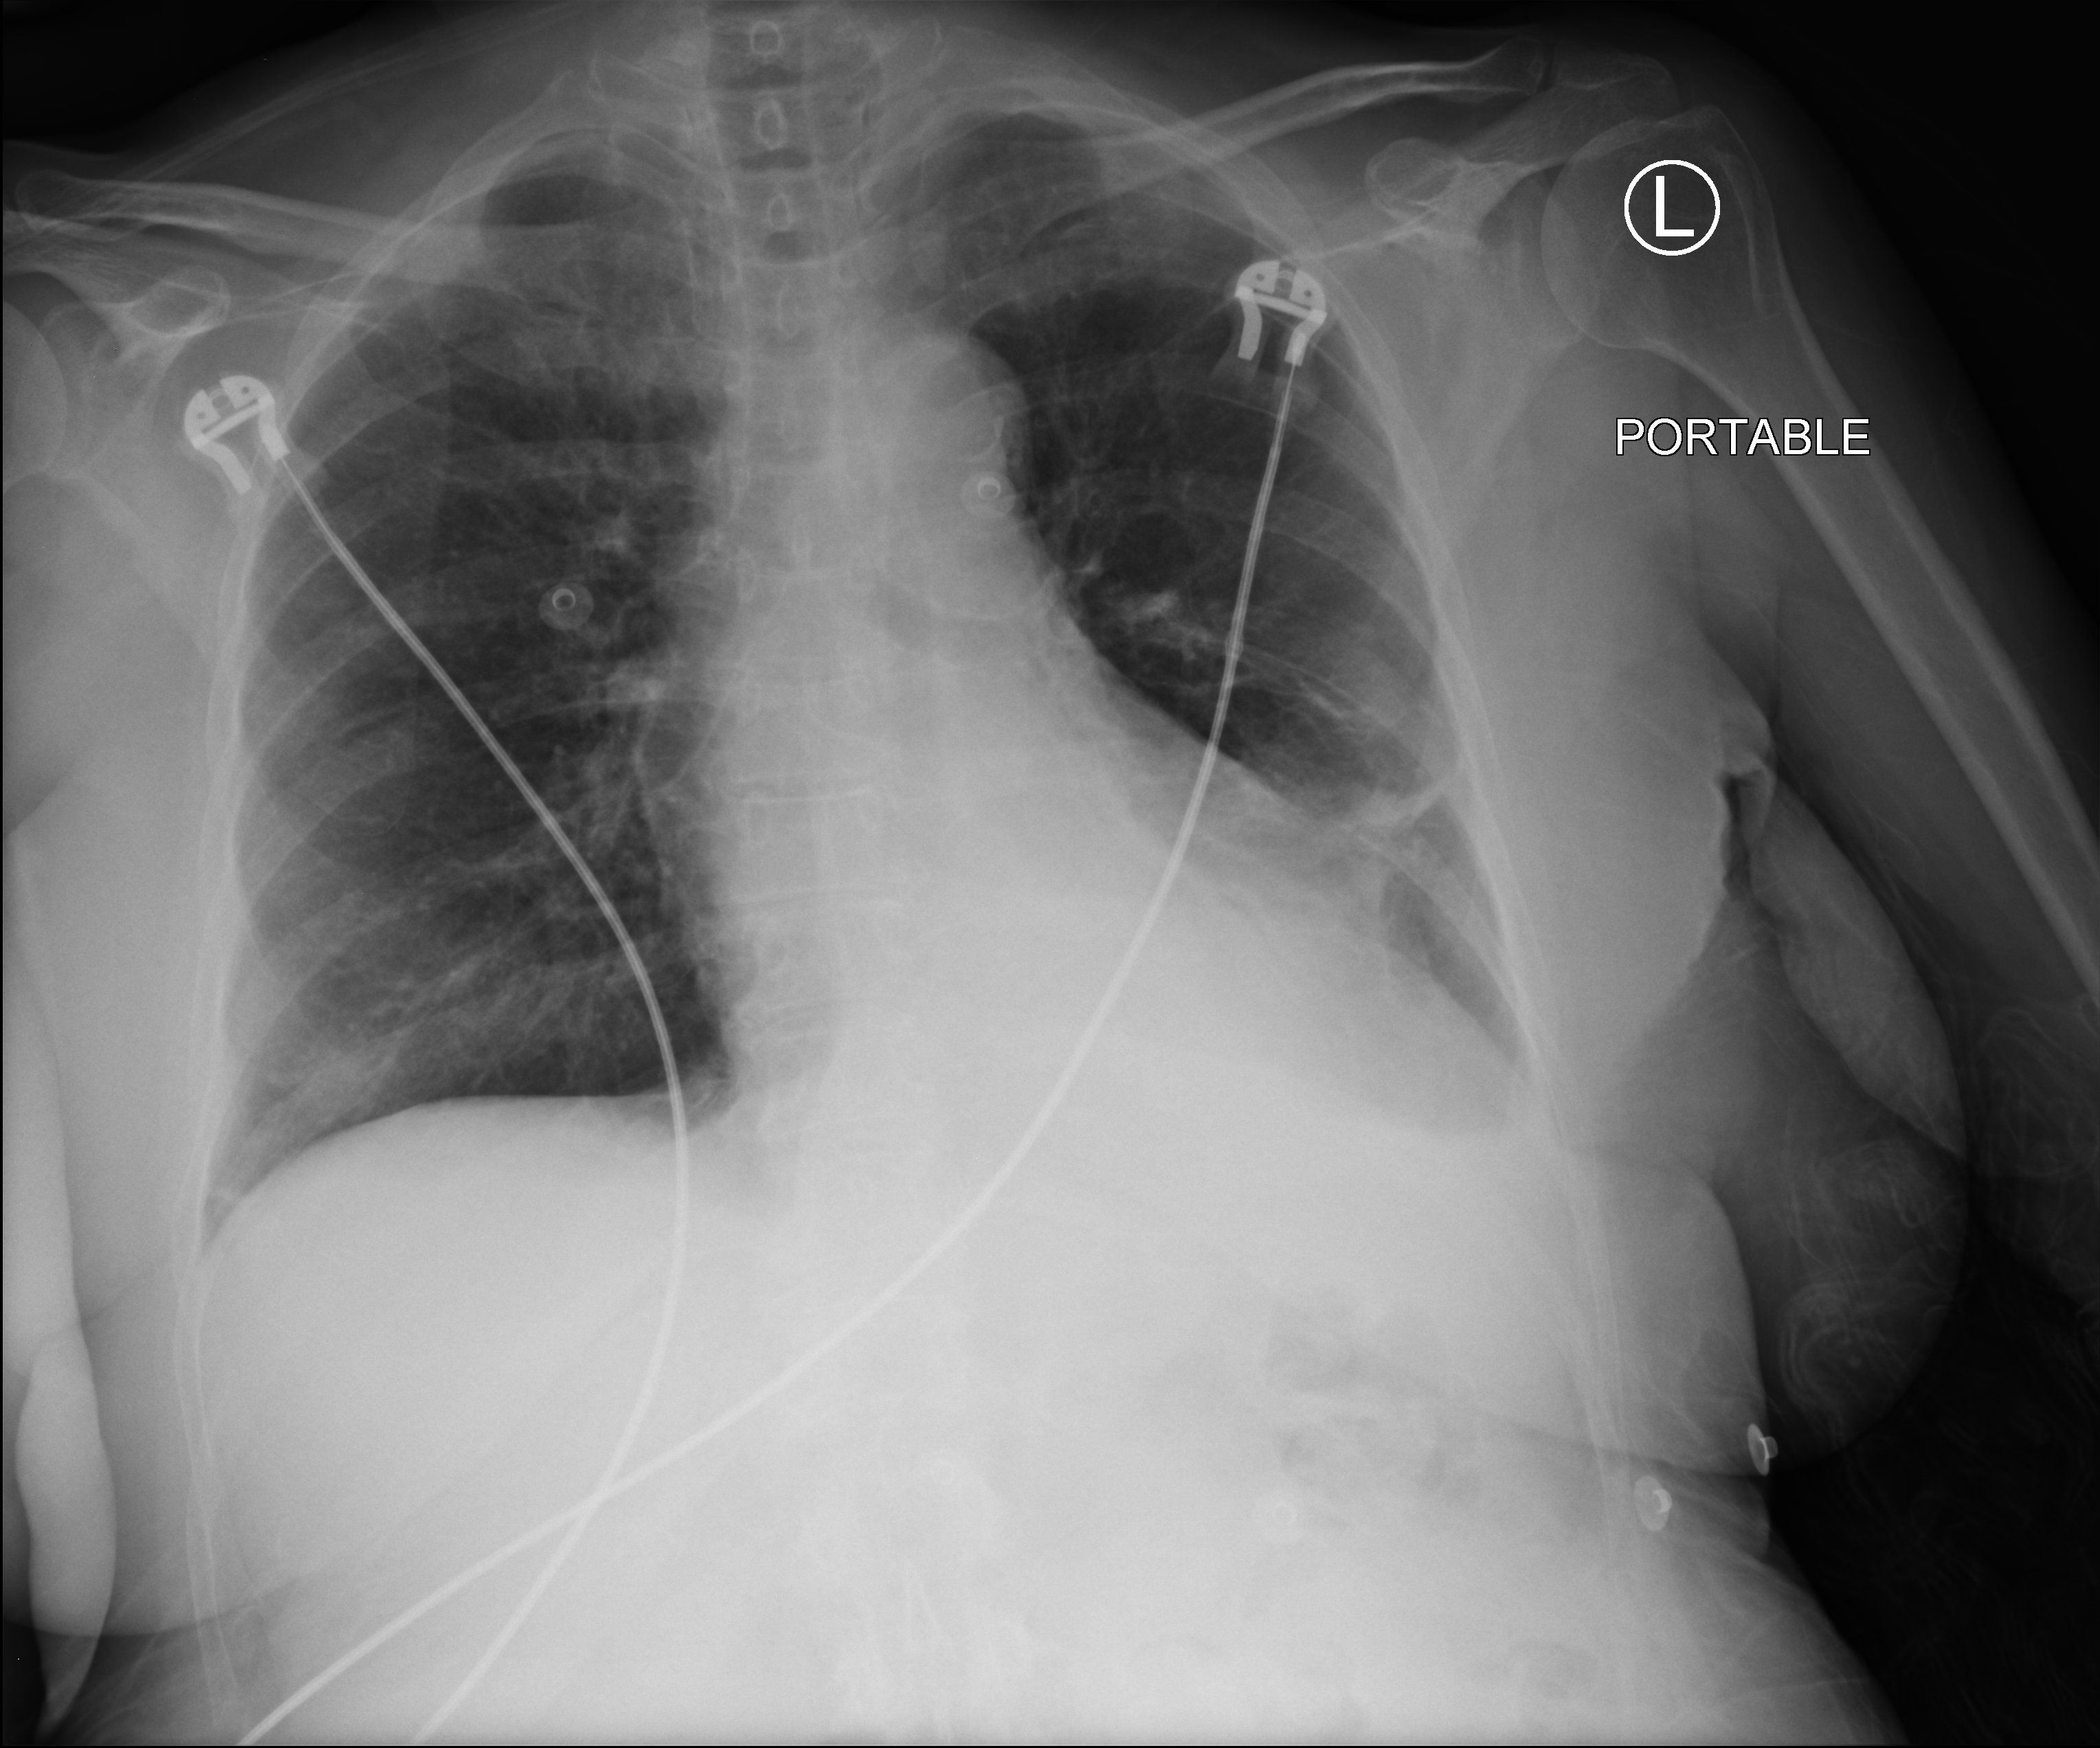
Portable chest radiograph; anteroposterior (AP) projection. Female patient hospitalised with COVID-19, age 75–90 years.
From the hospital-stay record, not from the radiograph (when in the stay this image was taken is not recorded): admitted to intensive care during this hospital stay: no; mechanically ventilated during this hospital stay: no.